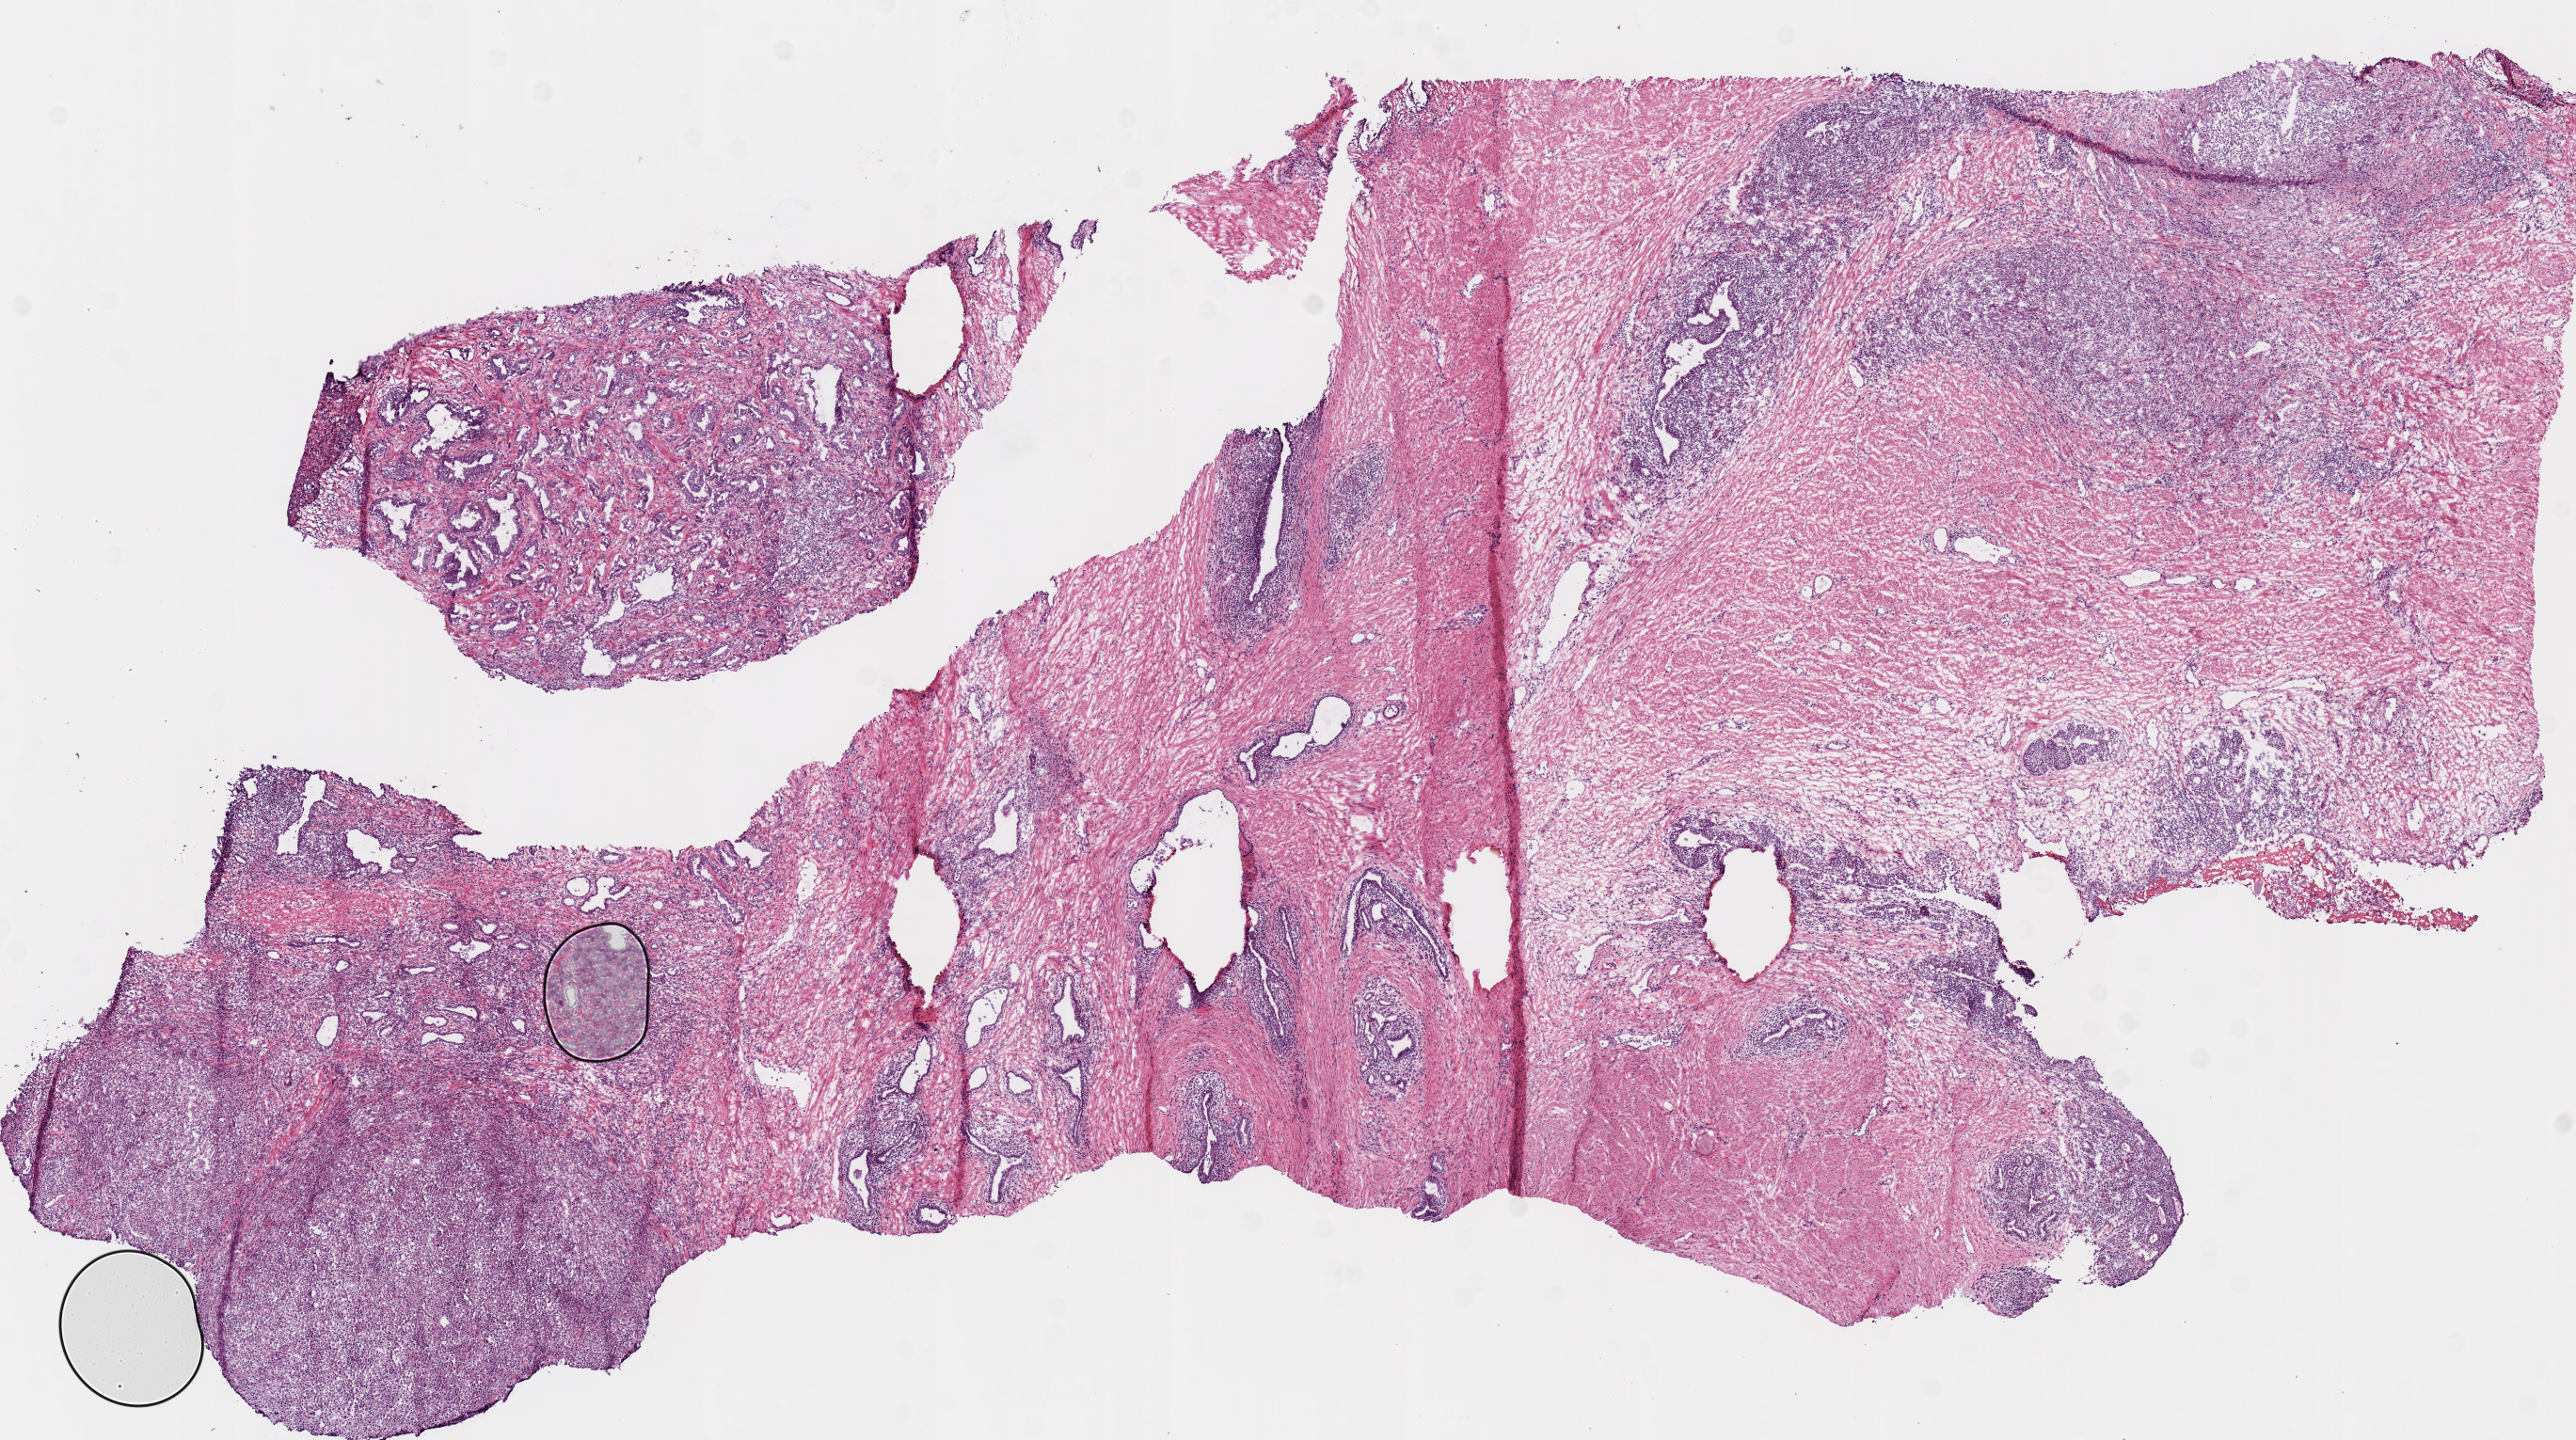
Digitized Hematoxylin and eosin (H&E) stained tissue section (whole slide), a low-resolution overview of the entire scanned area, about 10.8 x 6.1 mm (acquisition: 20x scan). Frozen section from the top of the tissue portion. Prostate, primary tumour sample. Male, age 58 years at initial diagnosis. Gleason score: 7 (4+3). Pathologist review of this section (percent, as recorded): tumour cells 75%, tumour nuclei 75%, normal cells 15%, stromal cells 10%, necrosis 0%.
* histologic diagnosis: Acinar cell carcinoma (prostate gland)
* lymph nodes positive (case pathology): 0 of 21 examined